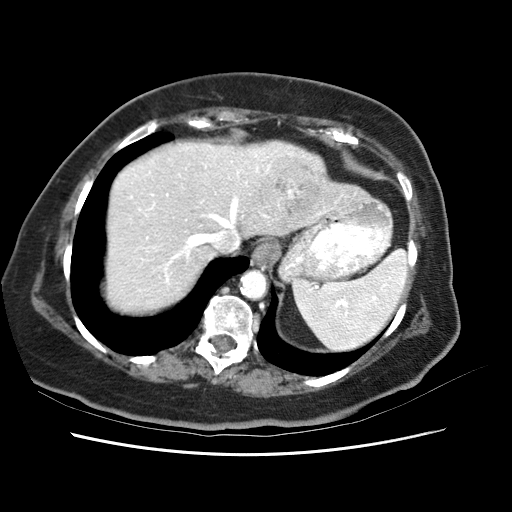
Contrast-enhanced abdominal CT (liver protocol), one axial slice; position 51 of 62 along the scan axis; reconstruction kernel STANDARD; 120 kVp; soft-tissue window (W 400 / L 40 HU); 2.5 mm slice thickness; 512 × 512 image matrix. Case-level facts recorded for this patient, not image findings: diagnosis: hepatocellular carcinoma (patient treated with transarterial chemoembolisation; whether this scan precedes or follows treatment is not stated here); TNM stage (as recorded): Stage-I; Child-Pugh class: B; tumour nodularity: uninodular.
Structures marked on this image (semi-automatically segmented with operator editing):
- abdominal aorta: box from (x=242, y=272) to (x=266, y=298) px
- liver parenchyma outside the tumour (the mass and vessels are separate outlines, so this box may not span the whole liver): (x=112, y=142)–(x=366, y=296)
- mass: (x=260, y=151)–(x=318, y=216)
- liver vessels: (x=132, y=160)–(x=328, y=274)